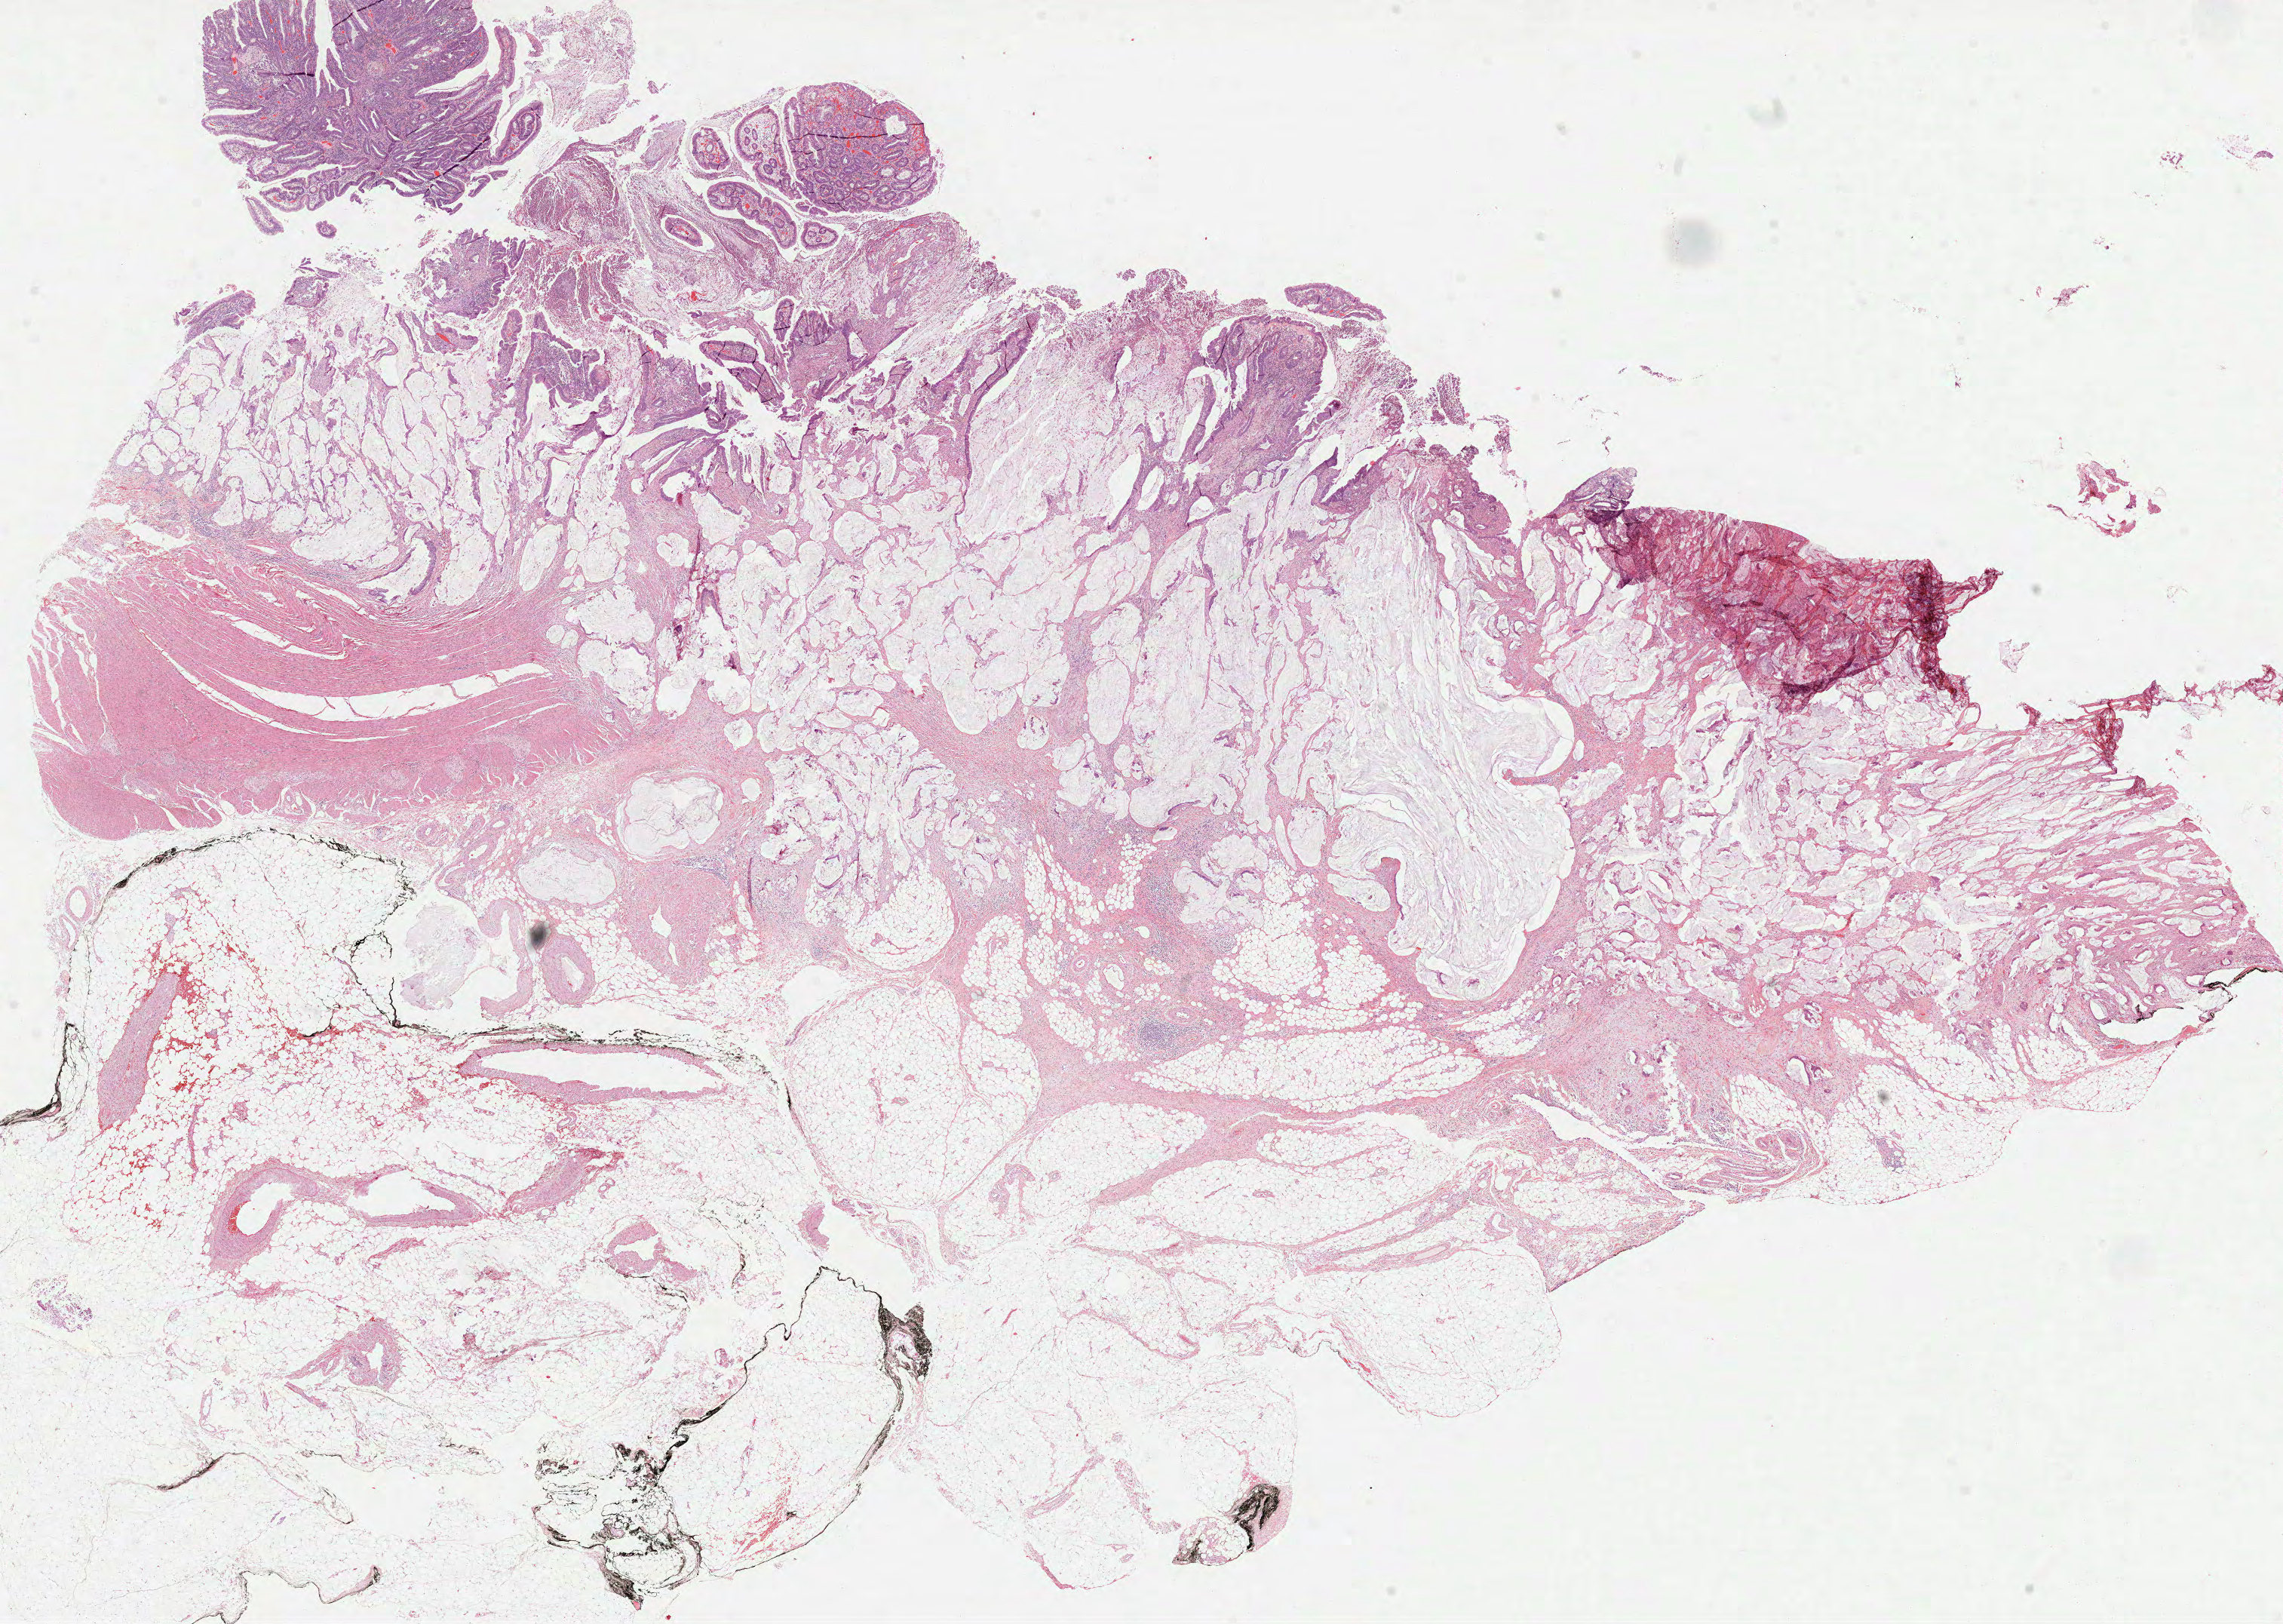
Digitized Hematoxylin and eosin (H&E) stained tissue section (whole slide) — low-resolution overview of the scanned area, about 24.4 x 17.4 mm (from a 40x scan); formalin-fixed paraffin-embedded (FFPE) diagnostic section; colon, primary tumour sample. Patient sex: female.
AJCC pathologic stage: IIA. TNM: T3 N0 M0. Pathologic diagnosis: Mucinous adenocarcinoma. Lymph nodes positive (case pathology): 0 of 15 examined.